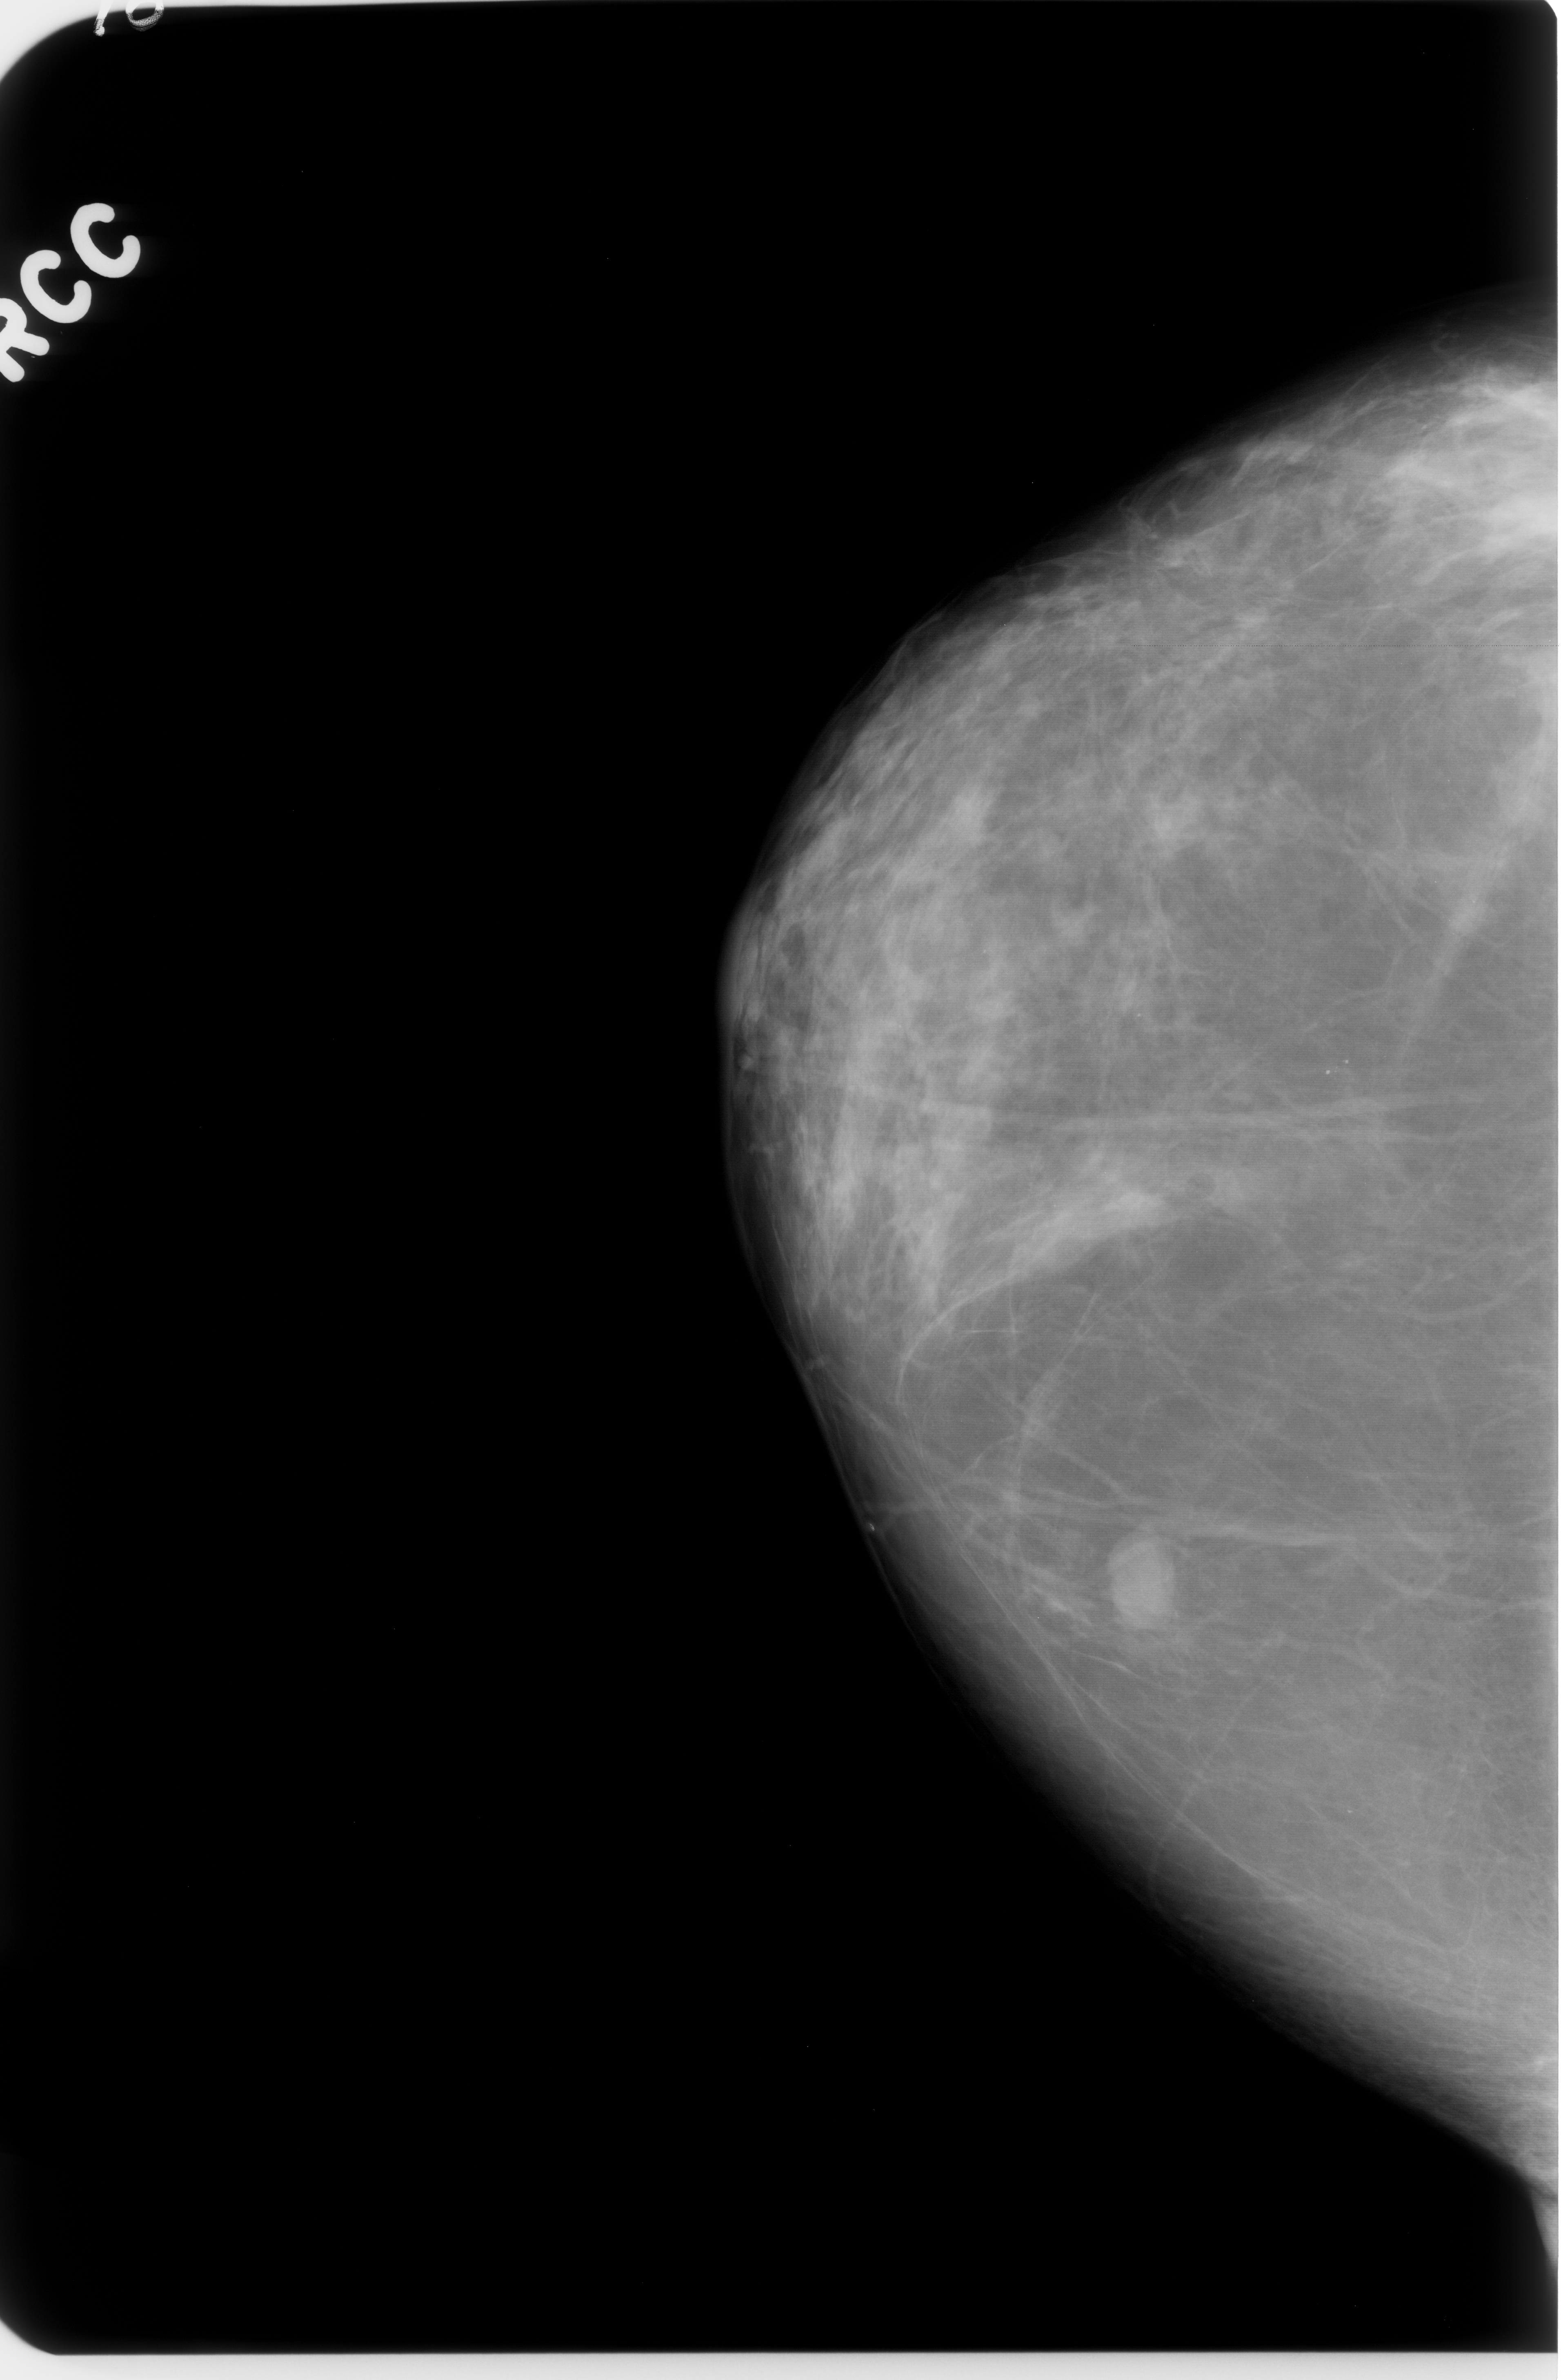
Mammogram (digitized film); right breast; craniocaudal (CC) view; BI-RADS breast density category 2 (scale 1–4).
Mass, shape oval, margins circumscribed; BI-RADS assessment category 4; pathology result (as recorded, not read from the image): benign.